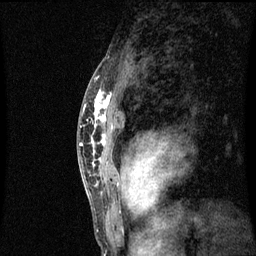
Breast MRI (dynamic contrast-enhanced), one sagittal slice. Position 44 of 60 along the scan axis. Dynamic contrast-enhanced series, image 2 of 3 at this slice position (ordered by acquisition). 1.5 T. TE 4.2 ms, TR 8.9 ms. 256 × 256 image matrix, field of view 200 × 200 mm. Female patient, age 50 years. From the clinical record (not read from this slice): setting: breast cancer imaged before/during neoadjuvant chemotherapy; receptor status: triple-negative.
Outlined on this slice (semi-automatically segmented with operator editing):
- analysis volume of interest (the breast-tissue region the enhancement analysis was run in; not a lesion): bounding box <84,80,119,171> (left, top, right, bottom; pixels)
- tumour enhancement mask (voxels above the 70 % enhancement threshold inside the analysis volume of interest): <92,90,113,165>